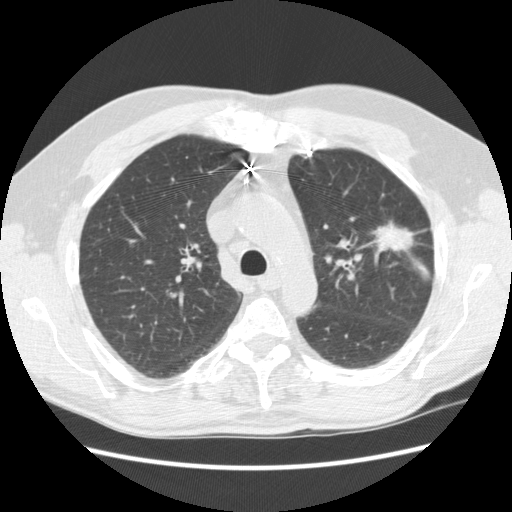
Chest CT (low-dose screening protocol), one axial image. First (baseline) screen. Lung window (W 1500 / L -600 HU). 120 kVp. 512 × 512 image matrix, field of view 362 × 362 mm. Male, age 72 years at enrolment. Former smoker at enrolment.
Expert reader's lesion annotation, bounding box [x1, y1, x2, y2] px = [358, 209, 428, 260]. Reader record for this screening exam (exam-level; its link to the box is not recorded): non-calcified nodule or mass ≥4 mm, left upper lobe, 25 × 18 mm, spiculated (stellate) margins, soft tissue attenuation. Official screen result: positive, change unspecified: nodule(s) >= 4 mm or enlarging nodule(s), mass(es), or other non-specific abnormalities suspicious for lung cancer. Participant outcome: lung cancer diagnosed 35 days after this screen — adenocarcinoma, NOS, left upper lobe, well differentiated (G1), stage IIIB (AJCC 6th edition), 25 mm at pathology.